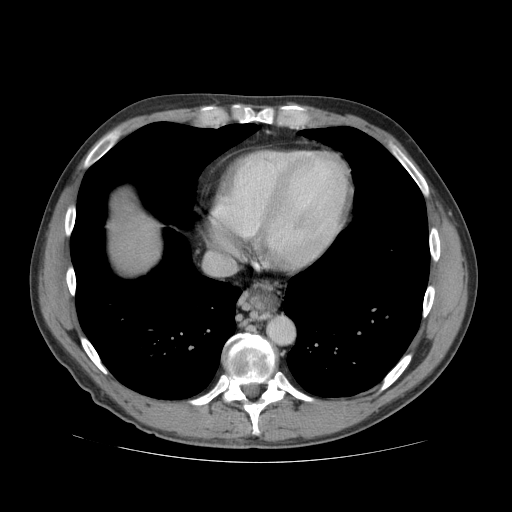
Contrast-enhanced abdominal CT (liver protocol), one axial slice. Position 73 of 81 along the scan axis. 140 kVp. Soft-tissue window (W 400 / L 40 HU). 2.5 mm slice thickness. 512 × 512 image matrix. Case-level facts recorded for this patient, not image findings: diagnosis: hepatocellular carcinoma (patient treated with transarterial chemoembolisation; whether this scan precedes or follows treatment is not stated here); TNM stage (as recorded): Stage-IVB; Child-Pugh class: B; tumour nodularity: multinodular.
Structures marked on this image (semi-automatically segmented with operator editing):
- liver parenchyma outside the tumour (the mass and vessels are separate outlines, so this box may not span the whole liver): bounding box (x1, y1, x2, y2) in pixels: (110, 202, 160, 272)